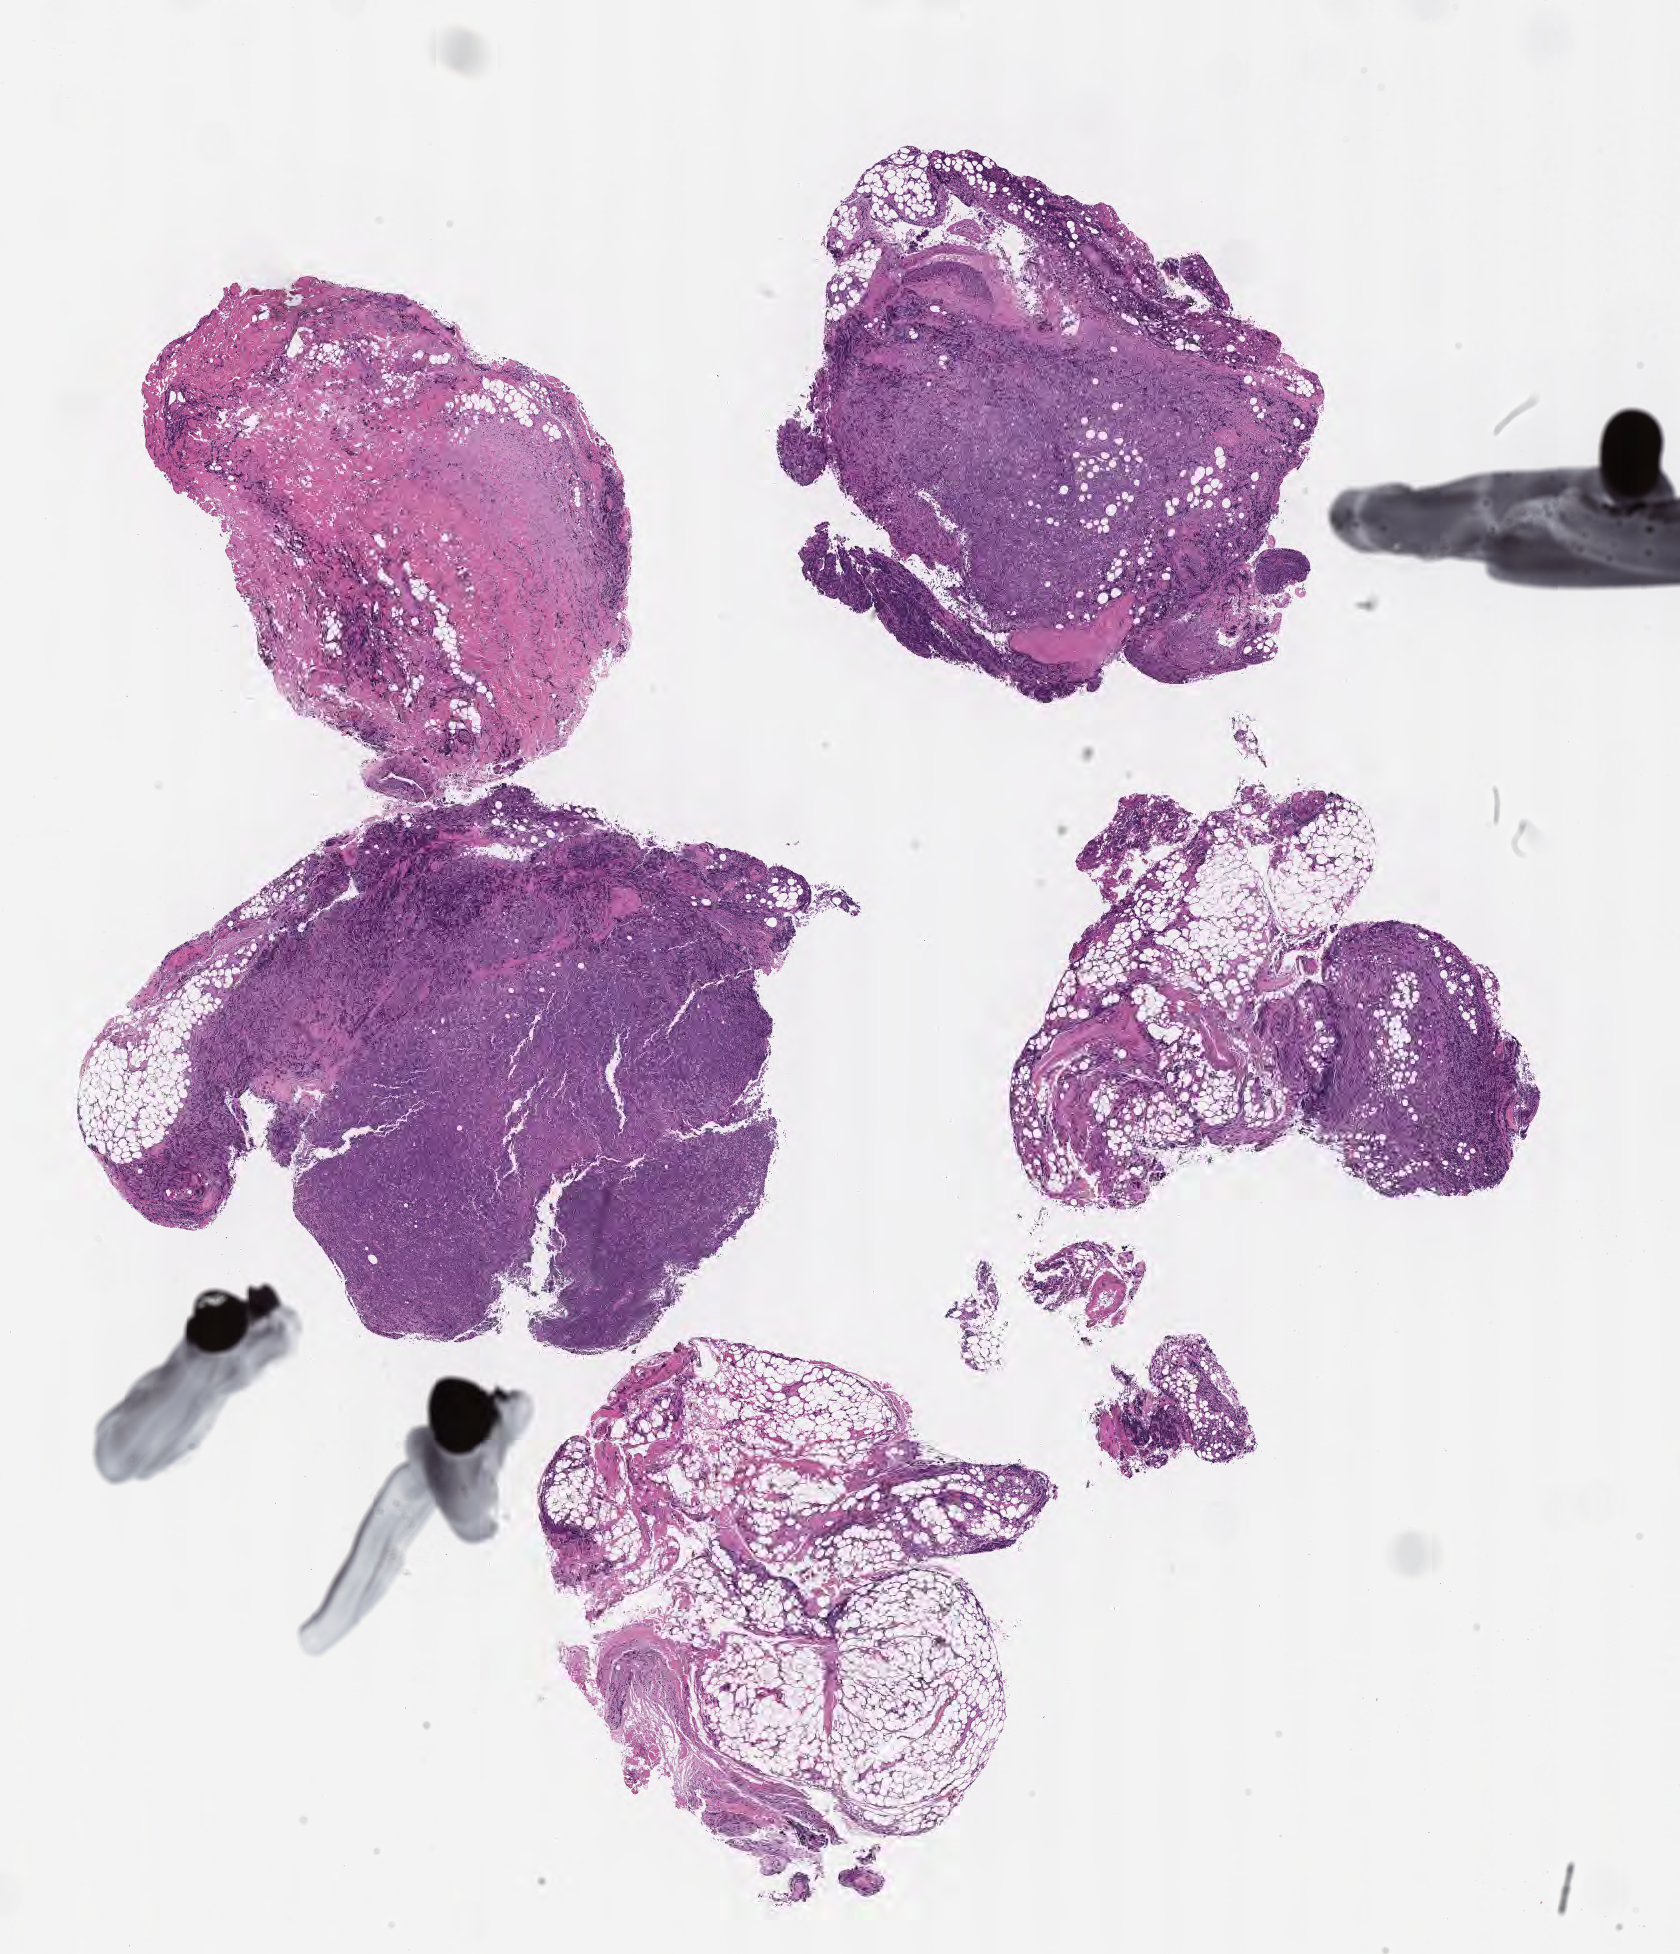
Whole-slide image, haematoxylin and eosin stain, shown as a low-resolution overview of the whole scanned area (about 13.6 x 15.8 mm). Tumor tissue. Patient male; 54 years old.
Histologic diagnosis: Burkitt lymphoma, NOS.